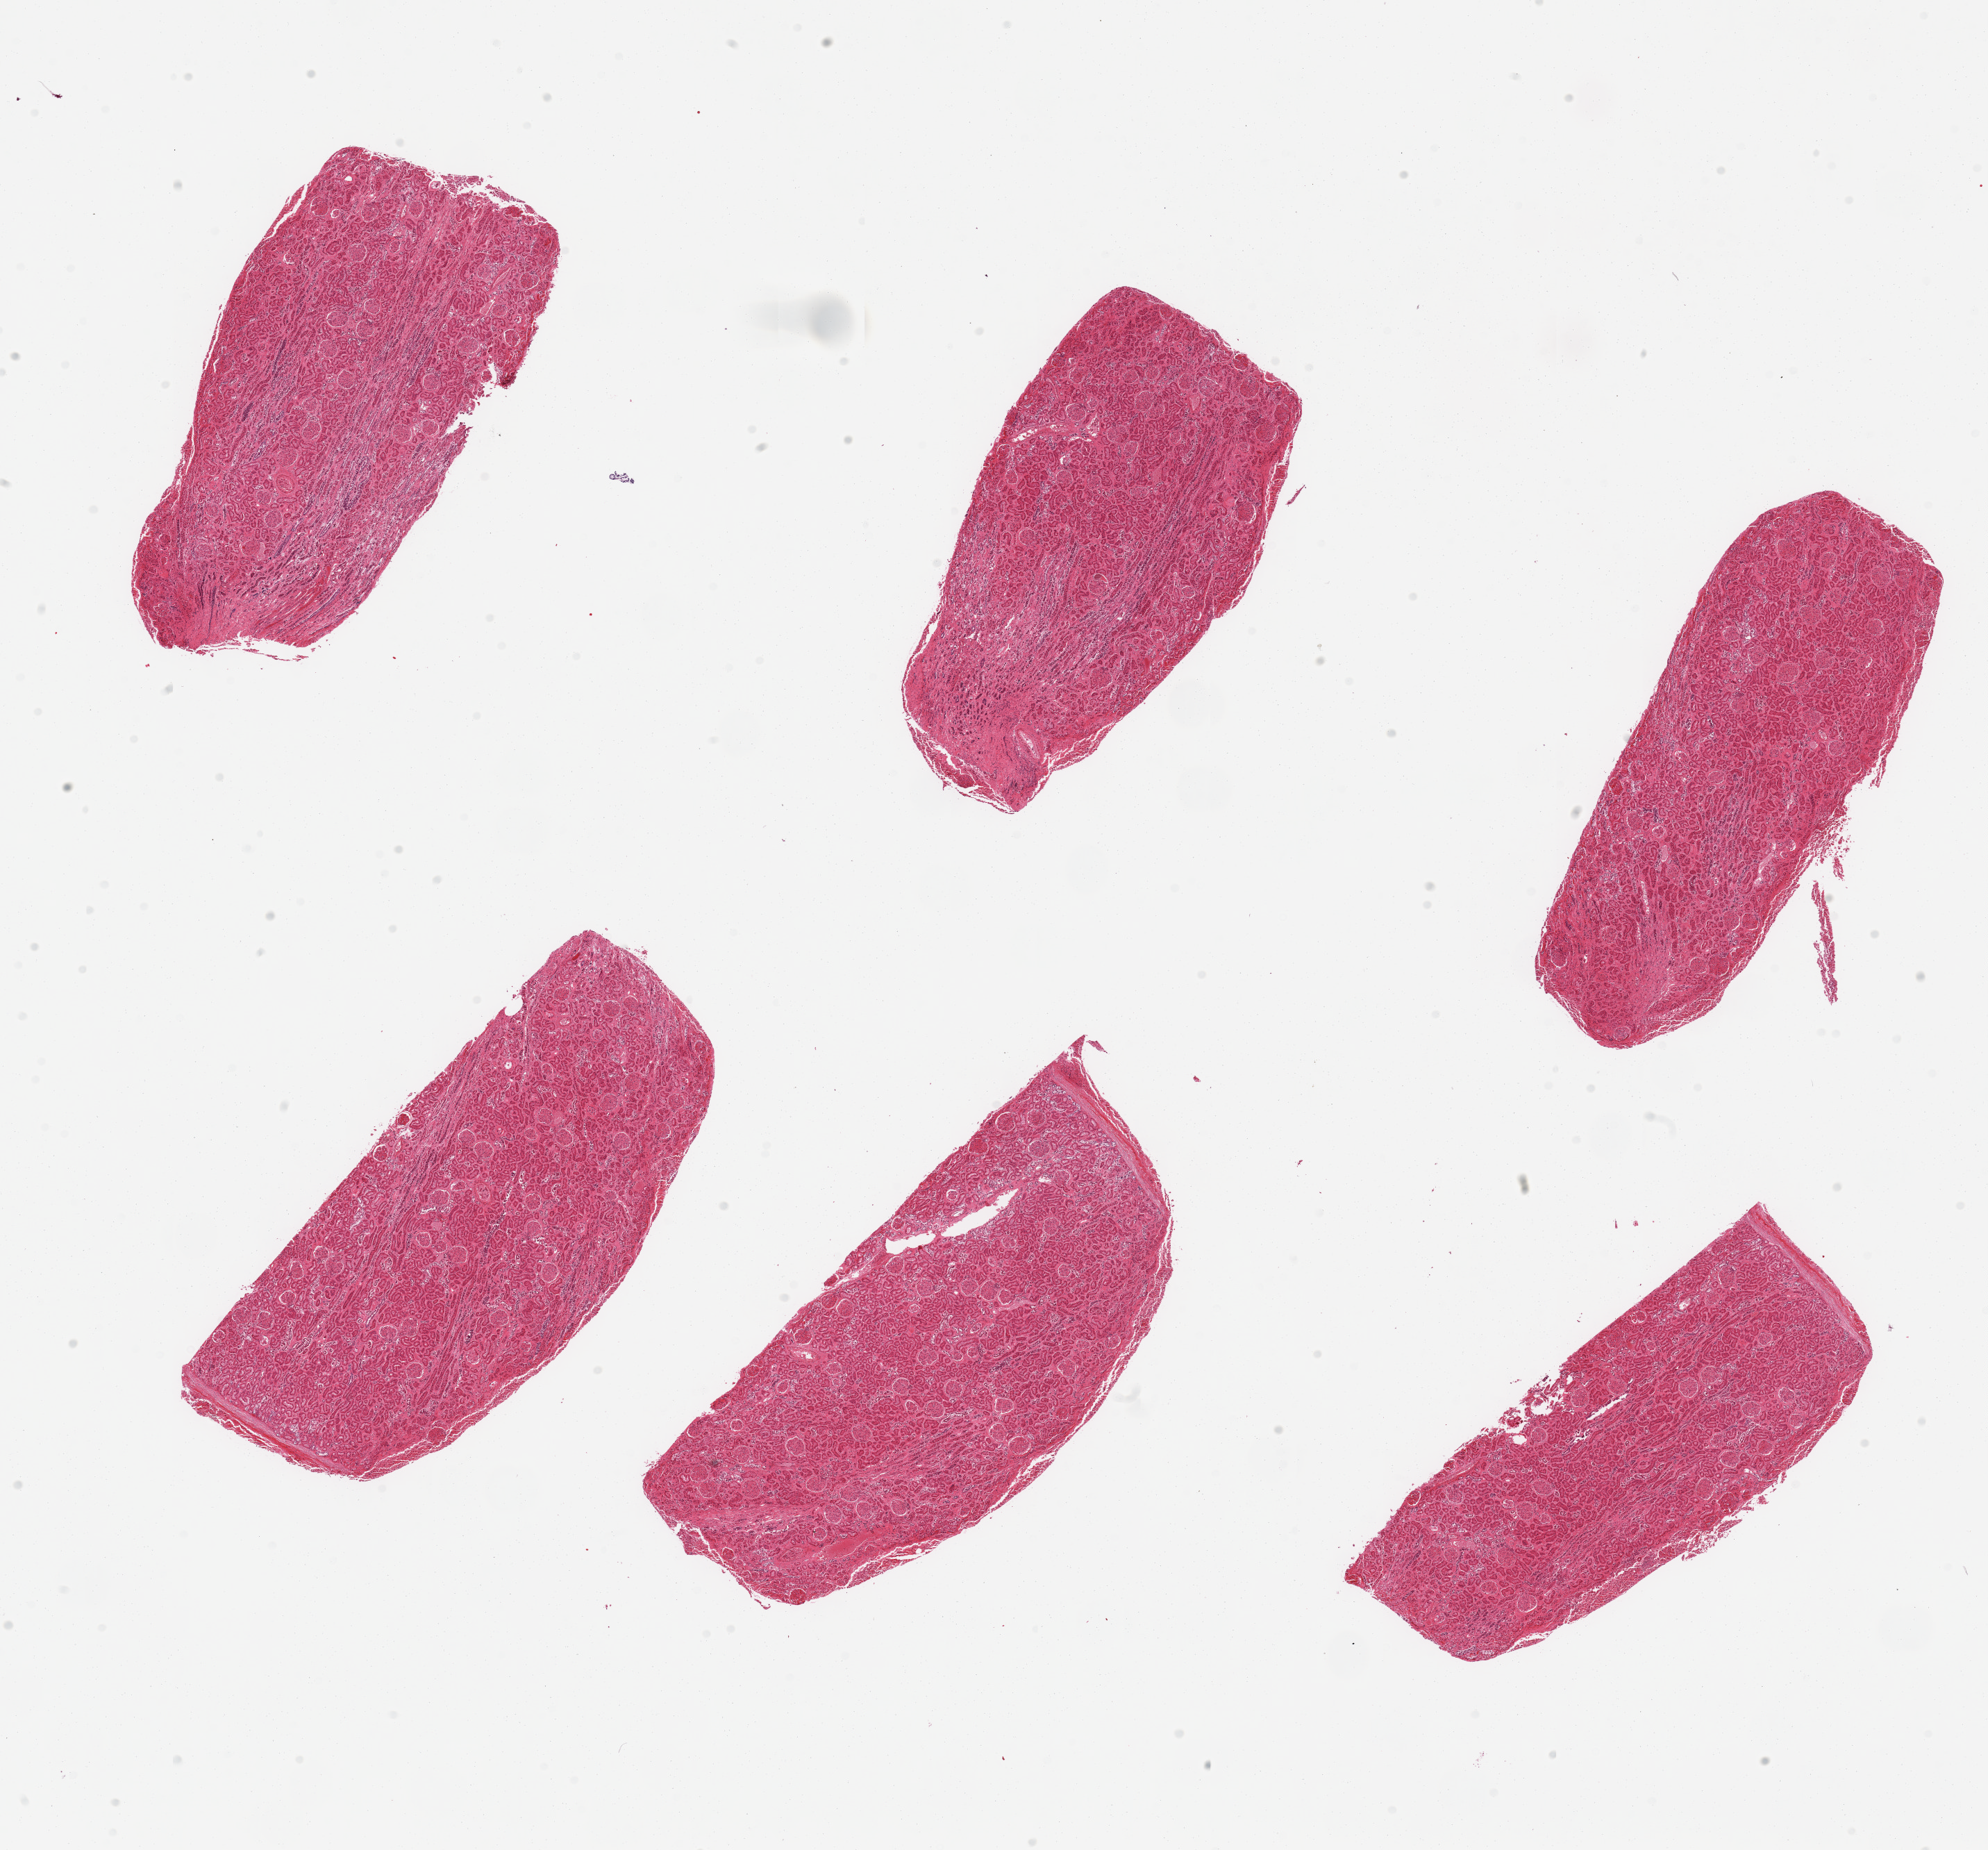
Whole-slide image, hematoxylin and eosin (H&E) stain, shown as a low-resolution overview of the whole scanned area (about 22.6 x 21.1 mm); PAXgene-fixed paraffin-embedded (PFPE) section; sampled site (target tissue): renal cortex; tissue donor sample. Donor: male.
Reviewer comment on this tissue sample: 6 pieces, glomeruli in all sections.